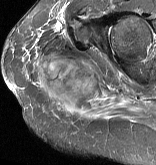
MRI of an extremity soft-tissue mass, one axial slice. Slice 40 of 57 in the series (ordered by position). STIR. MR volume resampled by the dataset authors to the PET/CT grid (not the native acquisition matrix). 156 × 165 image matrix. Female patient. From the clinical record (not read from this slice): histological type: epithelioid sarcoma with vascular differentiation; site of the primary tumour: right buttock.
Structures marked on this image (expert contour drawn on MRI and transferred to this co-registered scan by the dataset authors):
- gross tumour volume (mass): bounding box <38,55,98,108> (left, top, right, bottom; pixels)